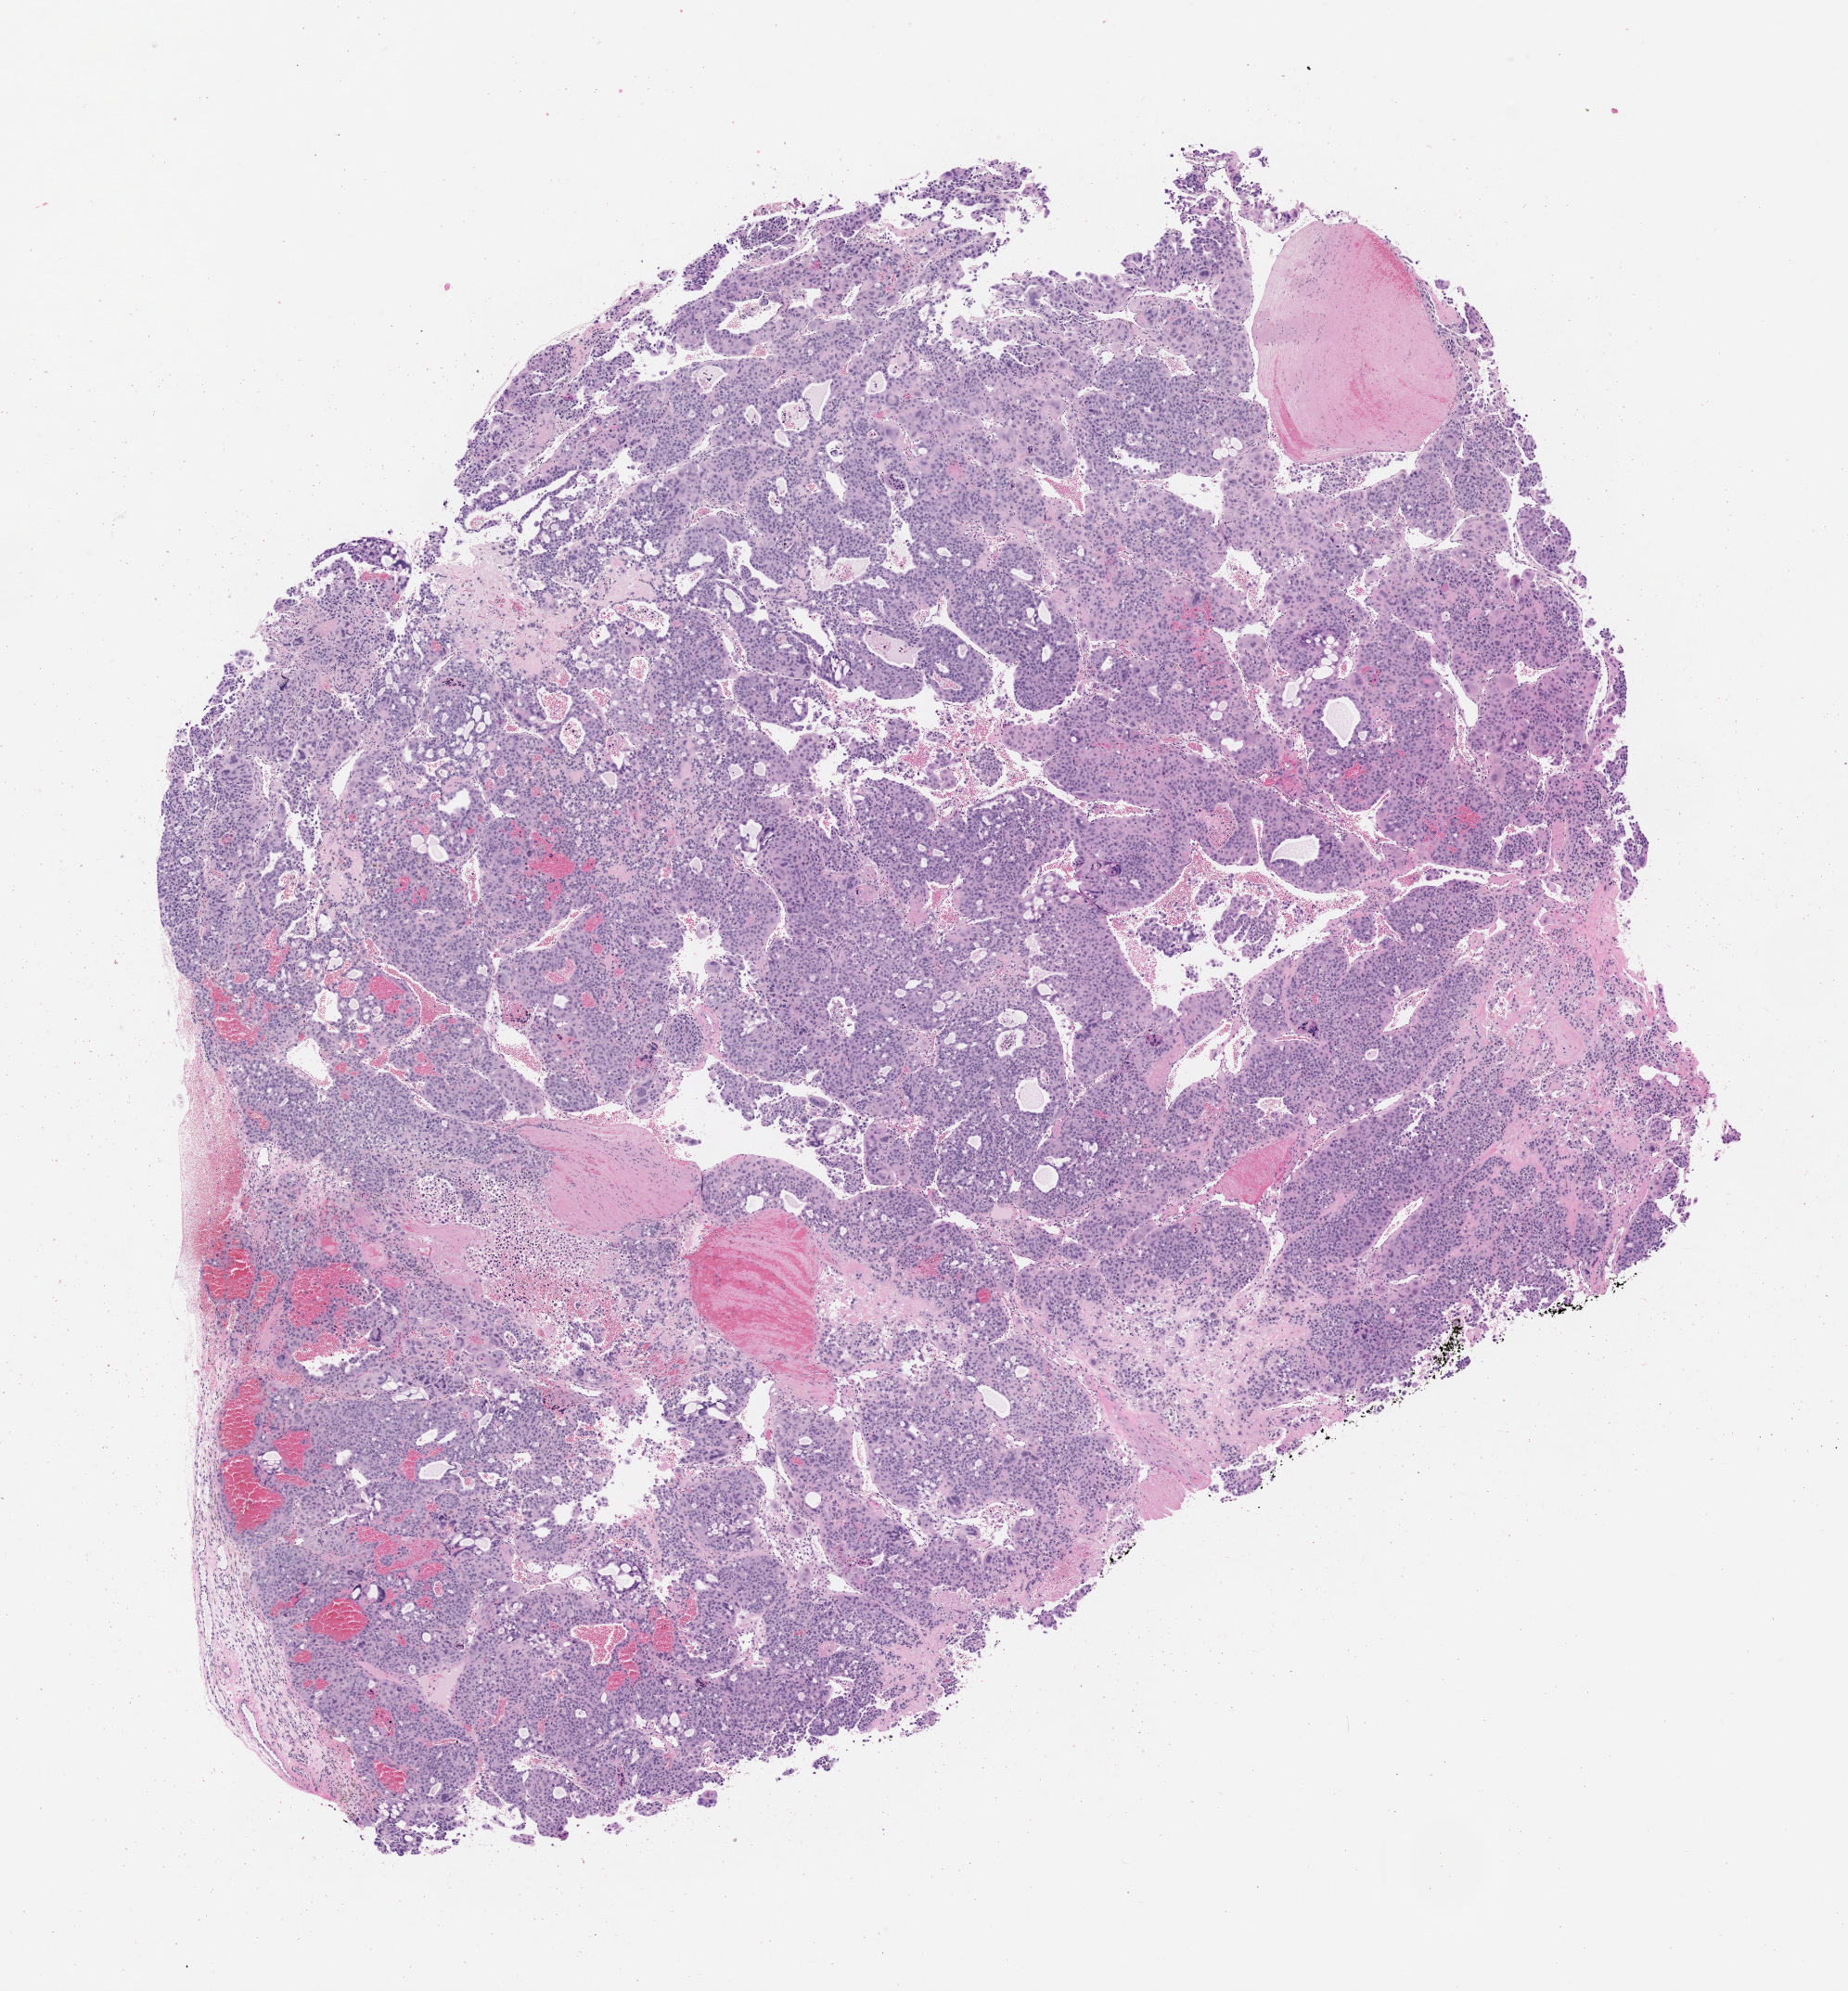
Whole-slide image, haematoxylin and eosin: patient-derived xenograft (human tumor grown in a mouse), passage 1 — a low-resolution overview of the entire scanned area, about 8.0 x 8.6 mm, formalin-fixed, paraffin-embedded (FFPE) tissue, tumor site category: bladder.
* originating patient diagnosis: Urothelial Carcinoma